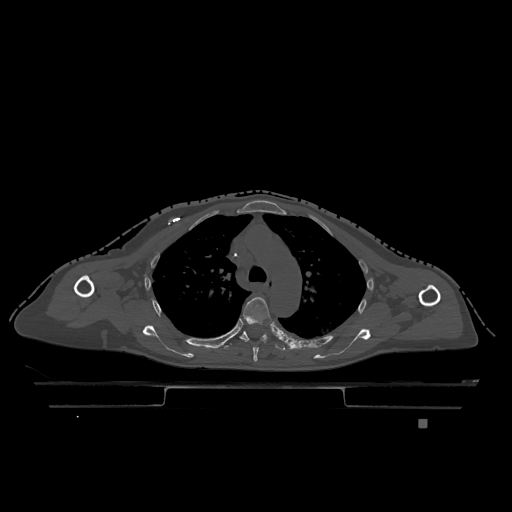
CT including the spine, one axial slice; slice 861 of 1317 in the series (ordered by position); bone window (W 1800 / L 400 HU); 0.5 mm slice thickness; 512 × 512 image matrix. Patient: female, 74 years. From the clinical record (not read from this slice): primary cancer: lung.
Structures marked on this image (semi-automatically segmented with operator editing):
- T4 vertebra: bounding box <240,297,272,362> (left, top, right, bottom; pixels)
- T5 vertebra: <221,331,286,351>